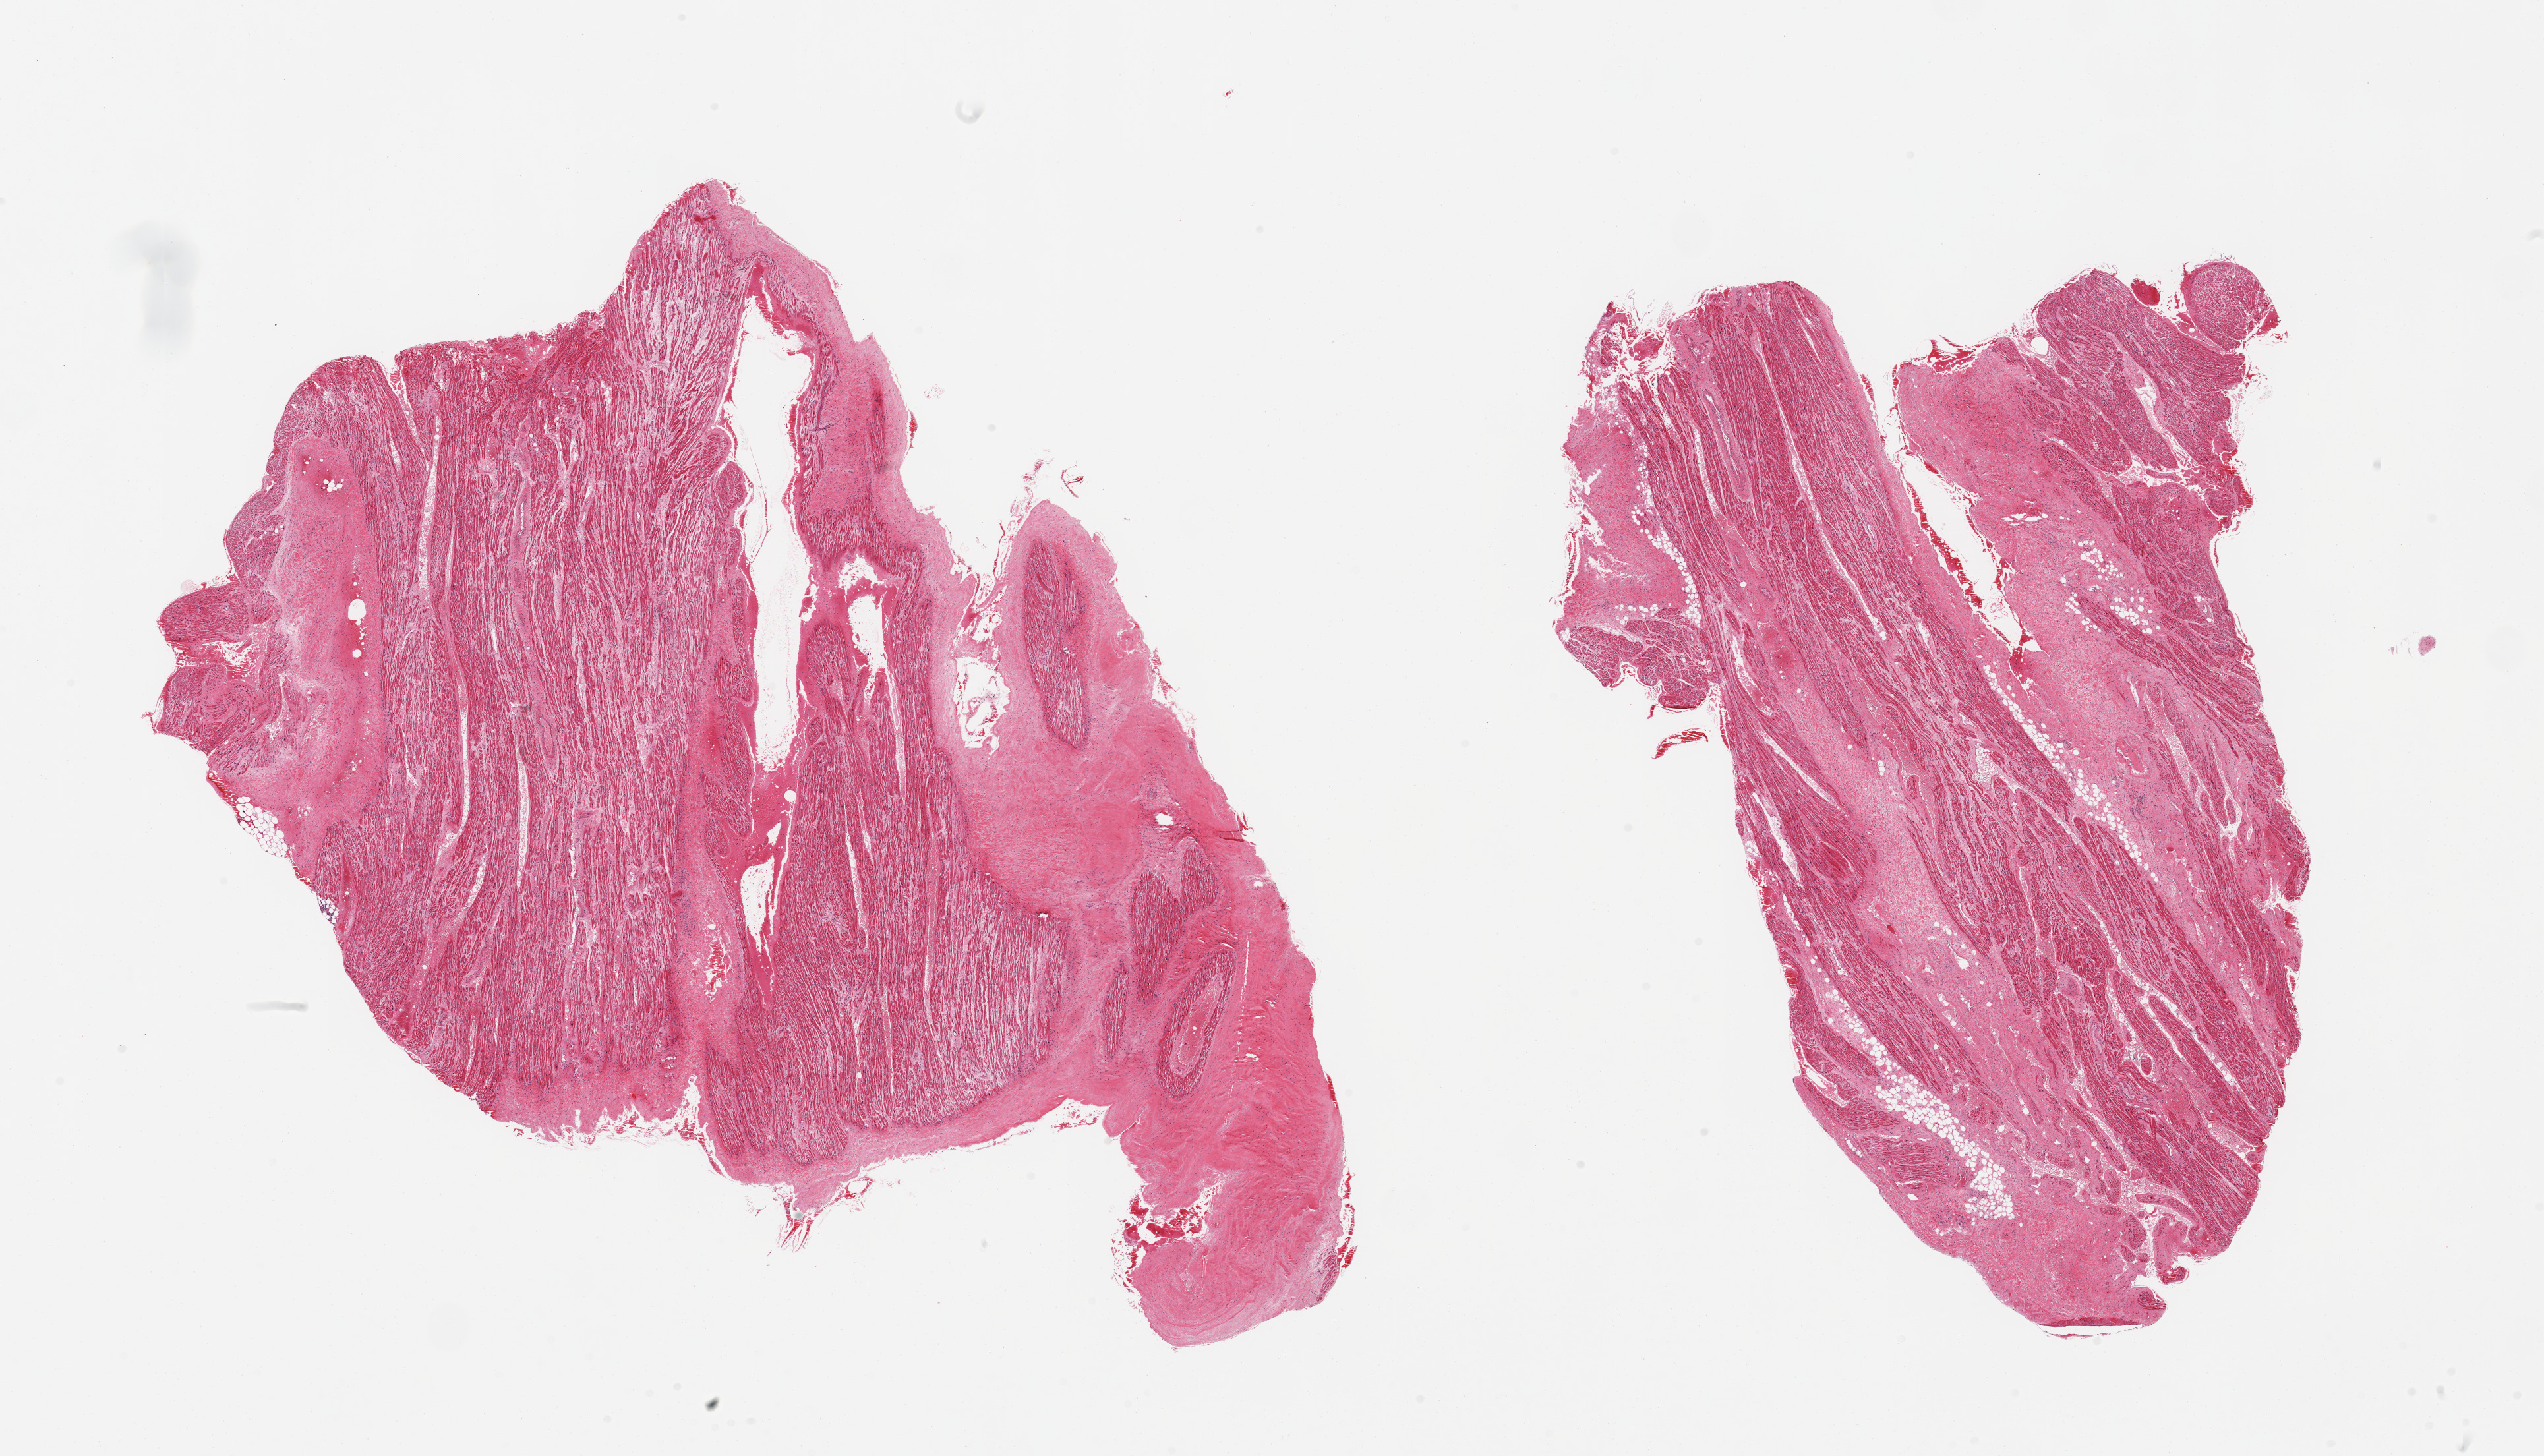
Digitized haematoxylin and eosin-stained section, low-resolution overview of the scanned area, about 30.5 x 17.5 mm; PAXgene-fixed, paraffin-embedded tissue; section of auricular appendage (target tissue); tissue donor sample. Donor: male.
Review note (as recorded): 2 pieces, no abnormalities.